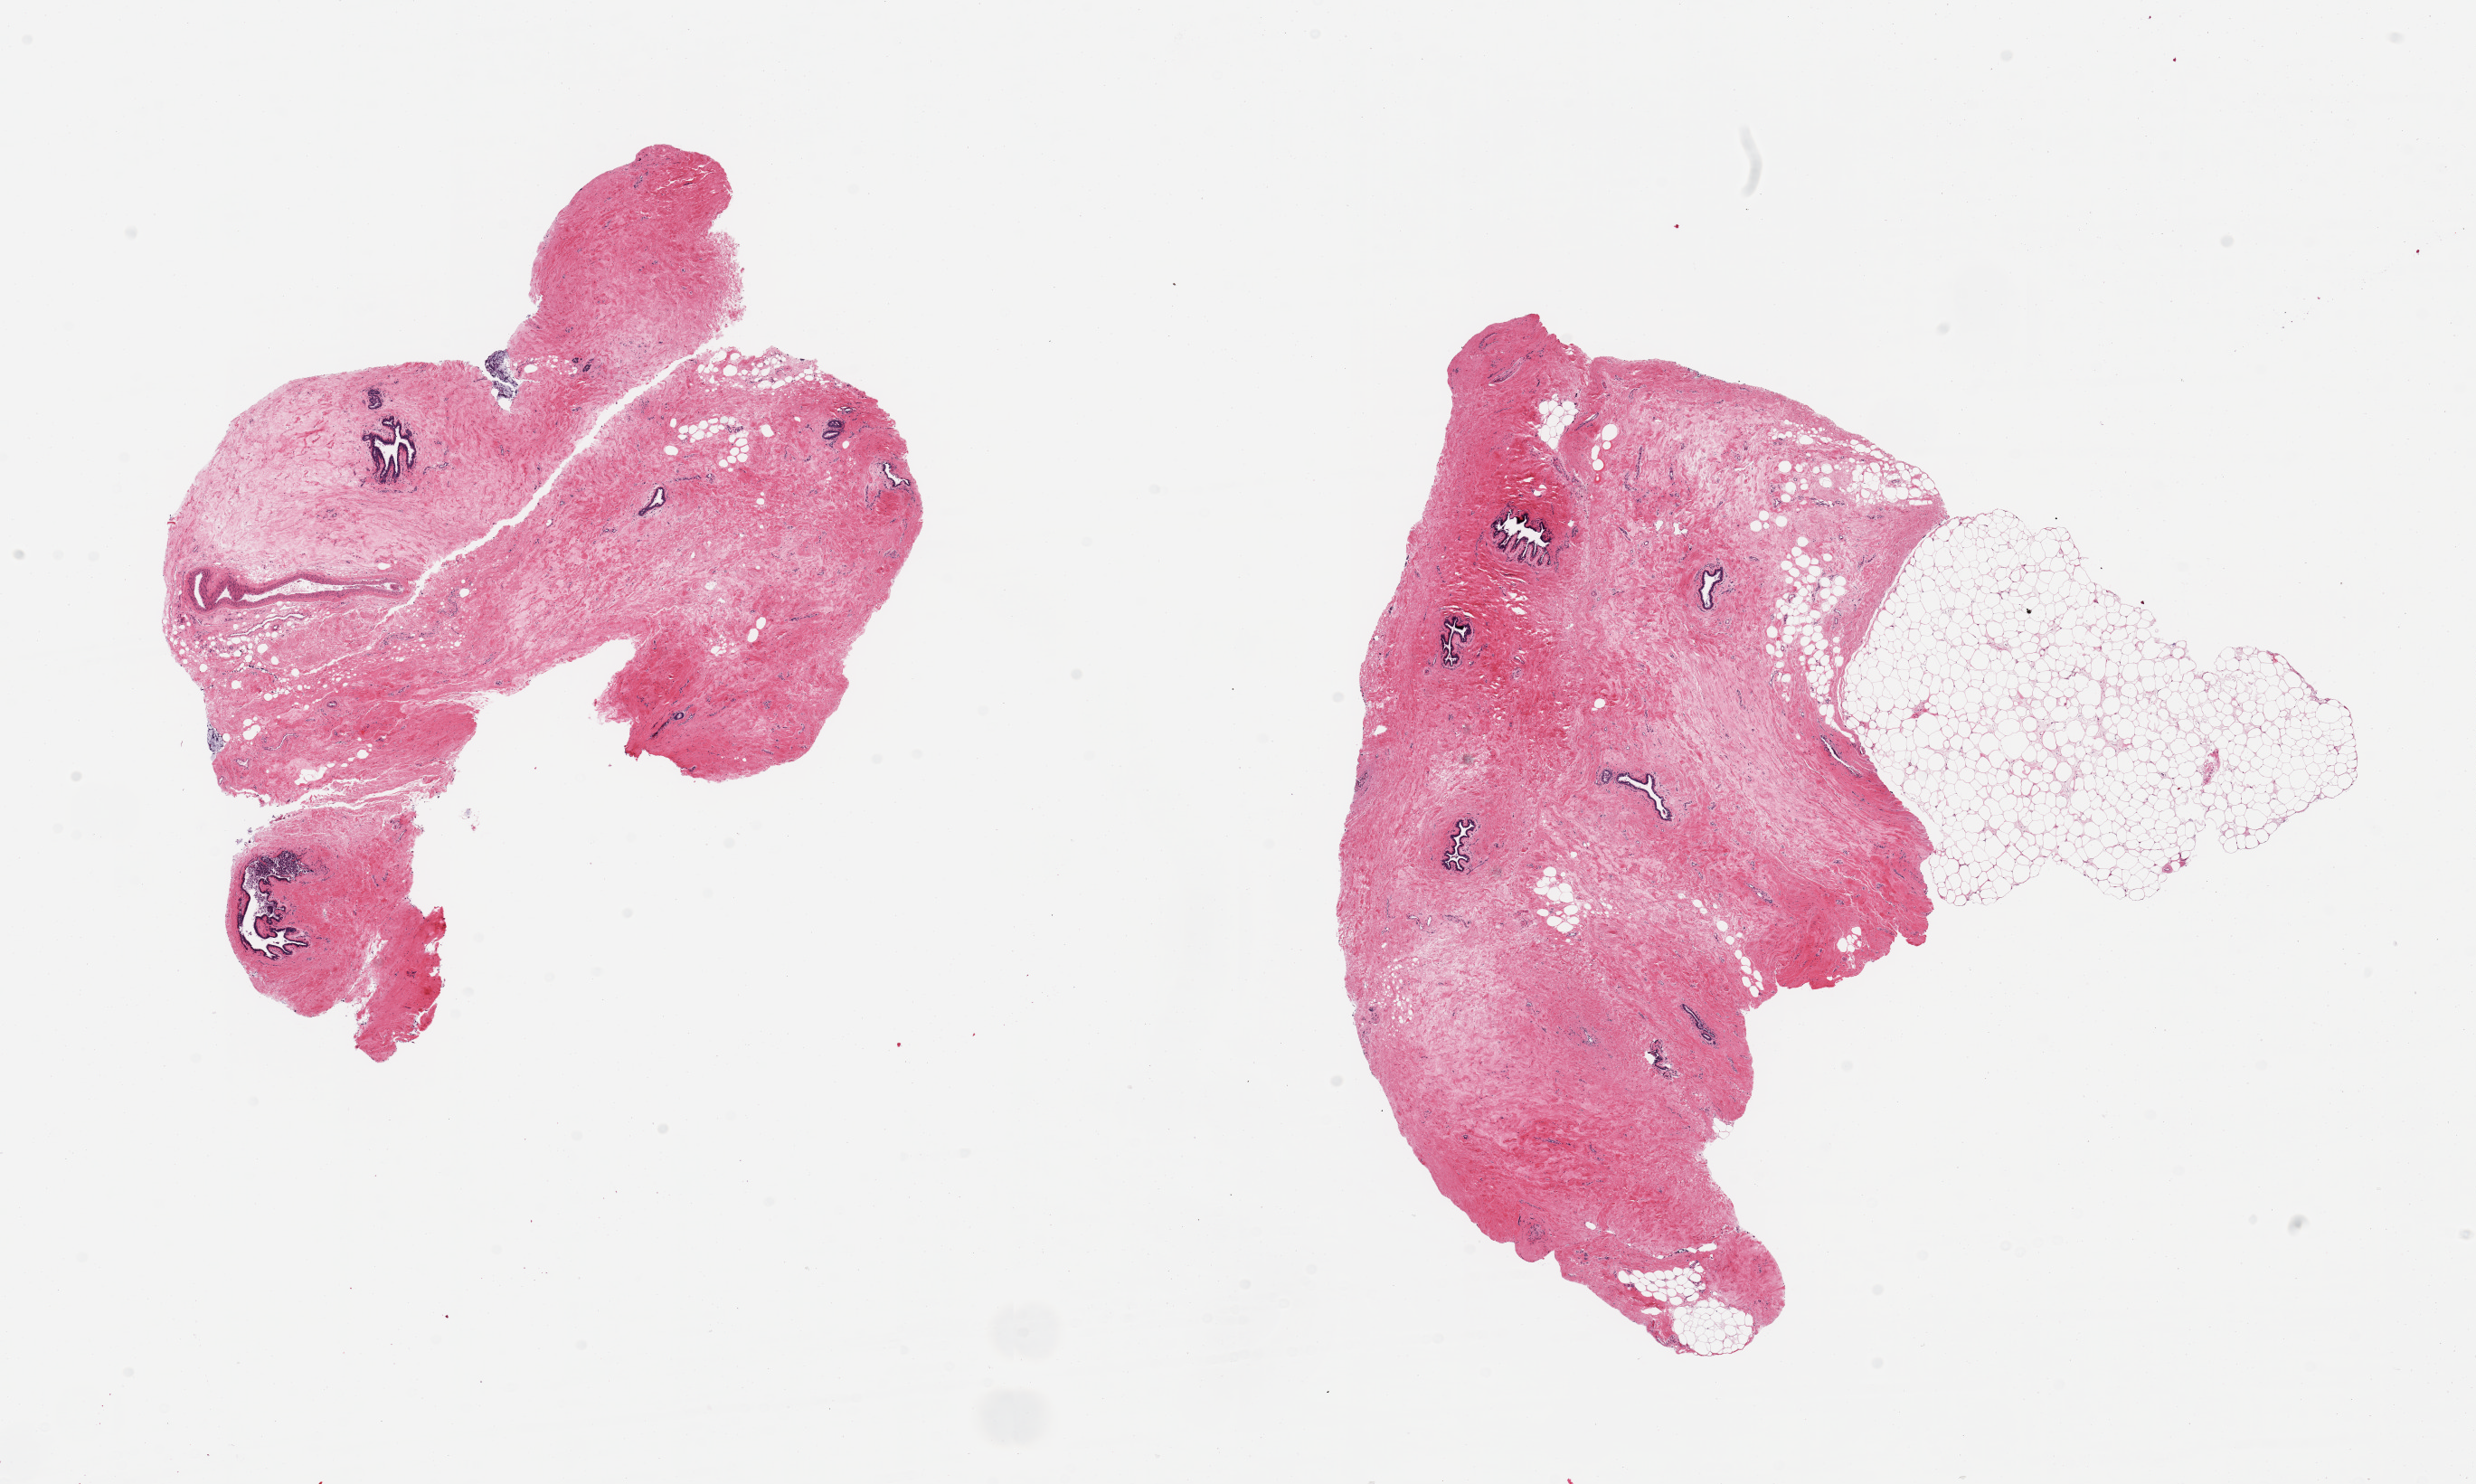
Whole-slide image, hematoxylin and eosin (H&E) stain — shown as a low-resolution overview of the whole scanned area (about 21.7 x 13.0 mm). PAXgene-fixed, paraffin-embedded tissue. Sampled site (target tissue): breast. Donor tissue sample. Male donor.
Reviewer comment on this tissue sample: 2 pieces, prominent gynecomastoid ductal and stromal hyperplasia.